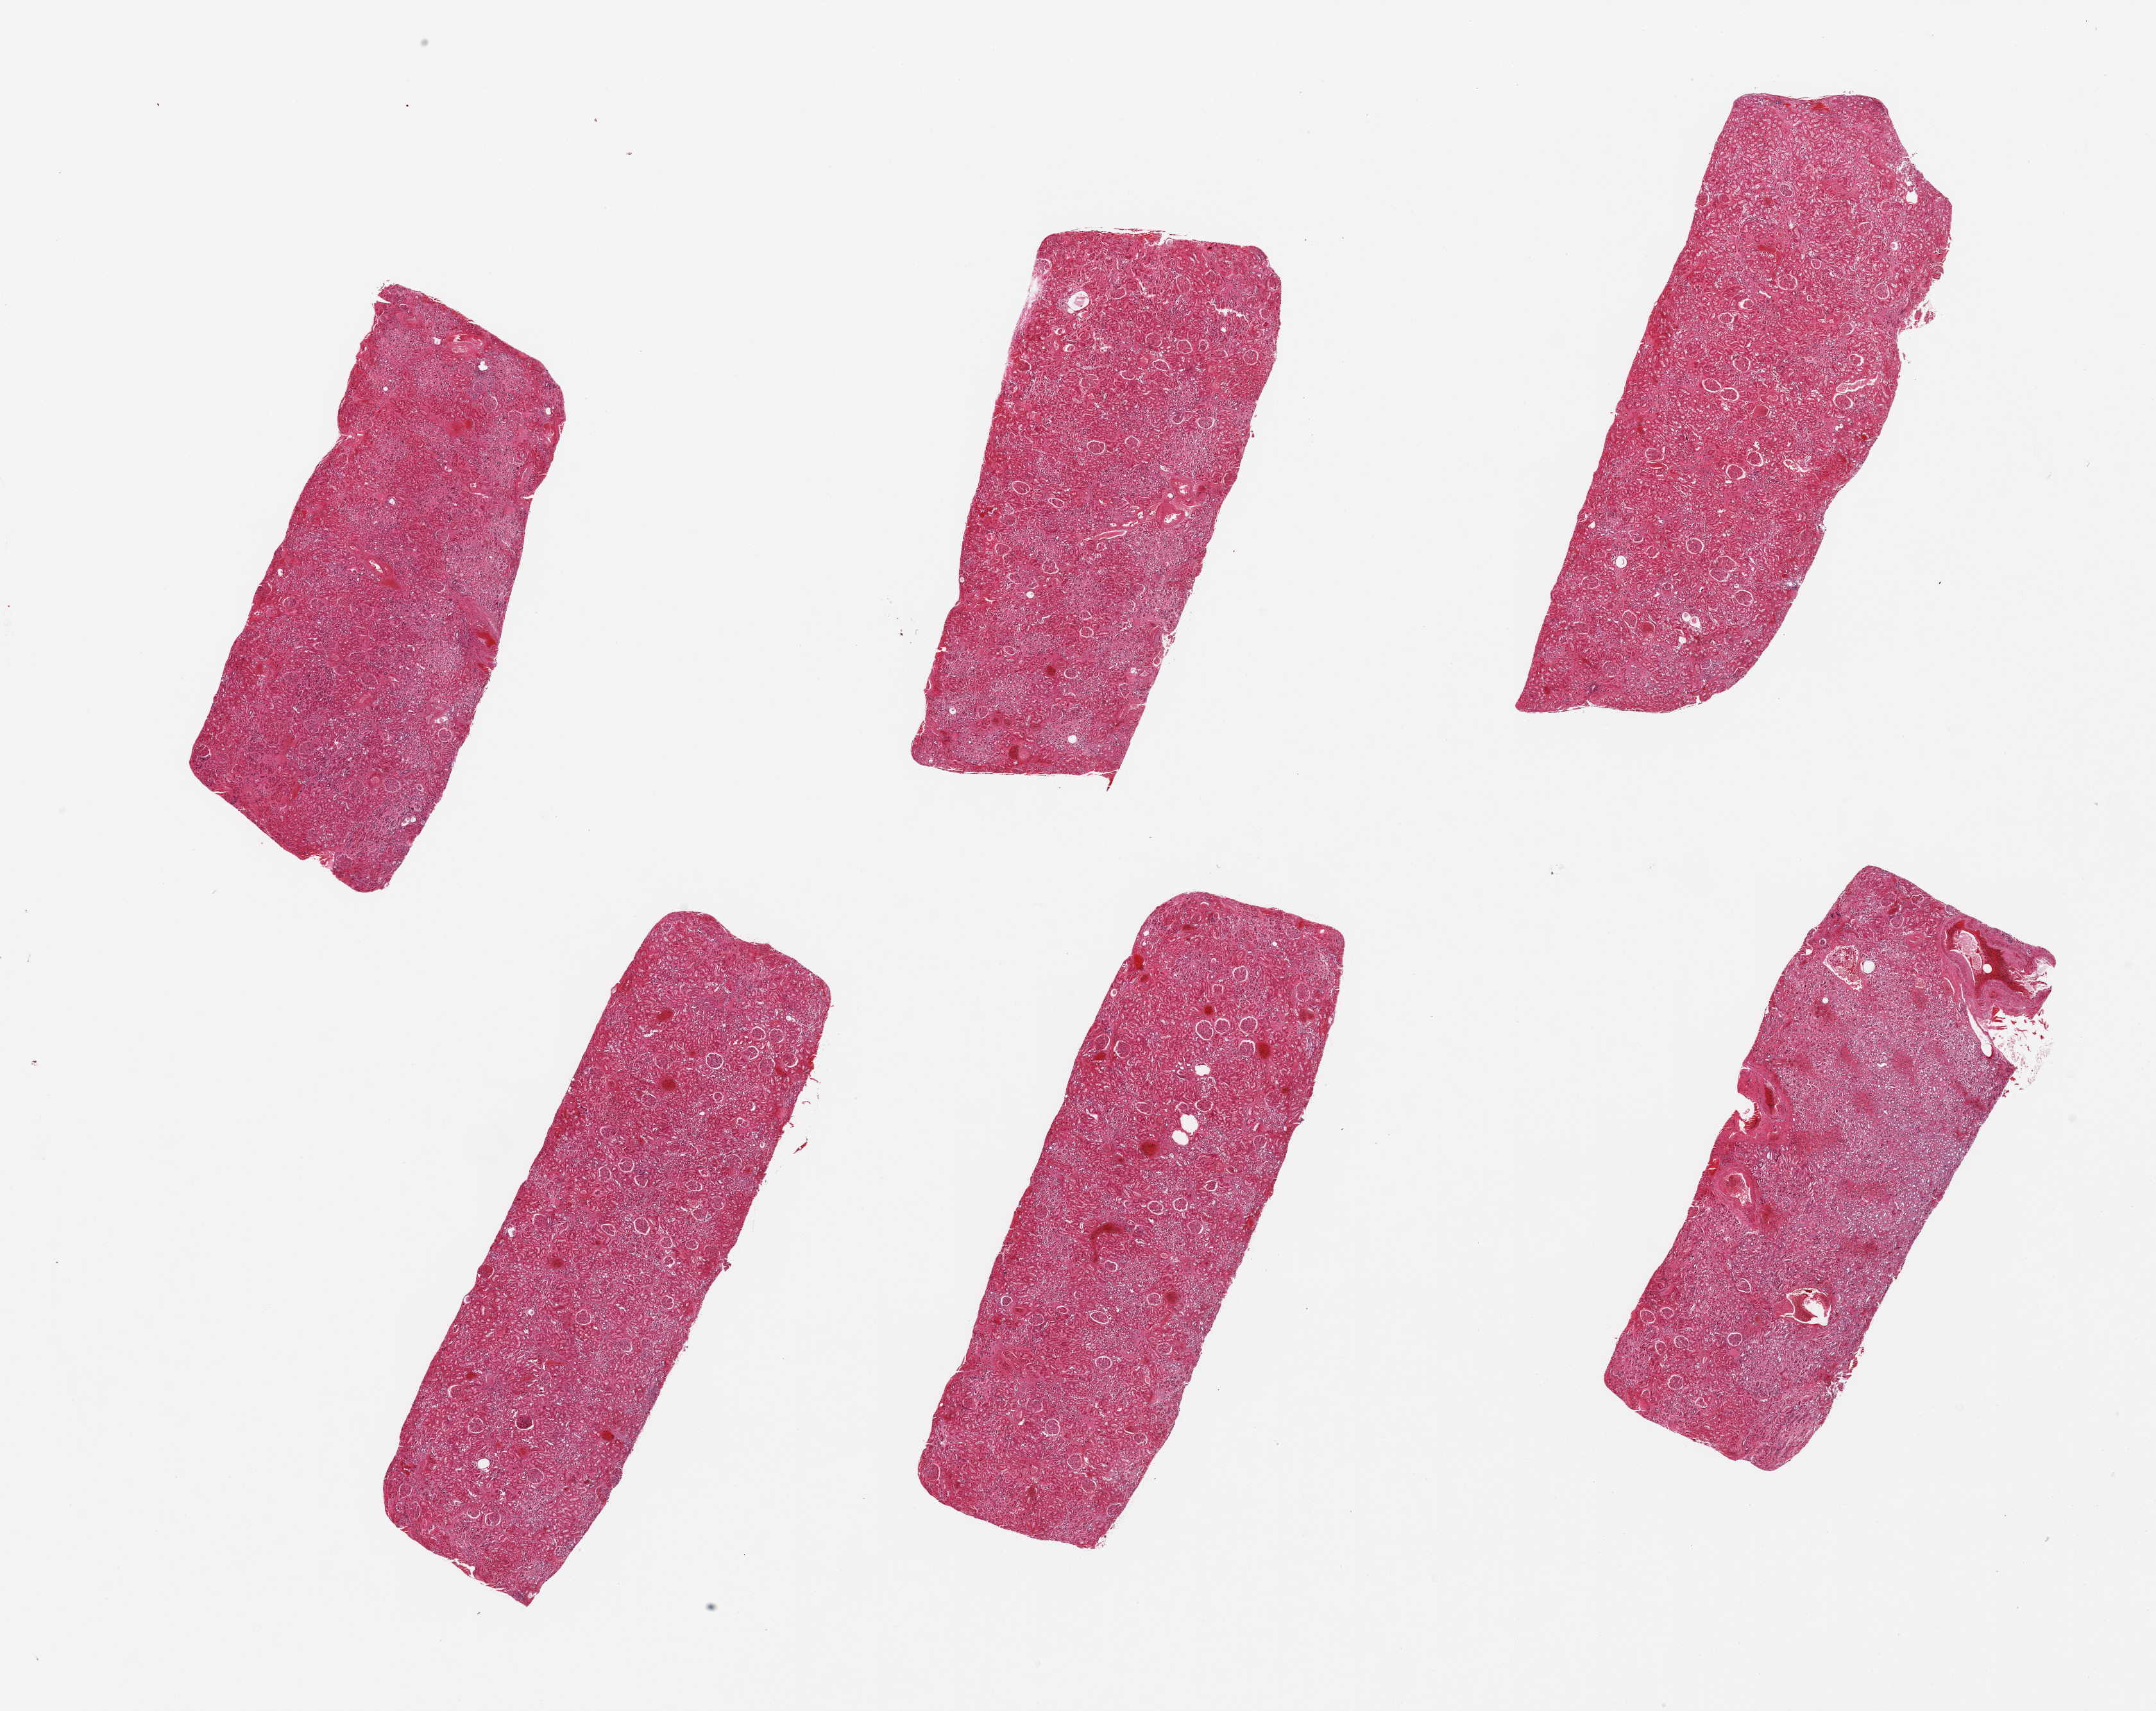
Whole-slide image, H&E stain — low-resolution overview of the scanned area, about 26.6 x 21.1 mm (acquisition: 20x scan); PAXgene-fixed, paraffin-embedded tissue; sampled site (target tissue): renal cortex; tissue donor sample. Male donor.
Reviewer comment on this tissue sample: 6 pieces; 5/6 are all cortex; 1 is mostly medulla.